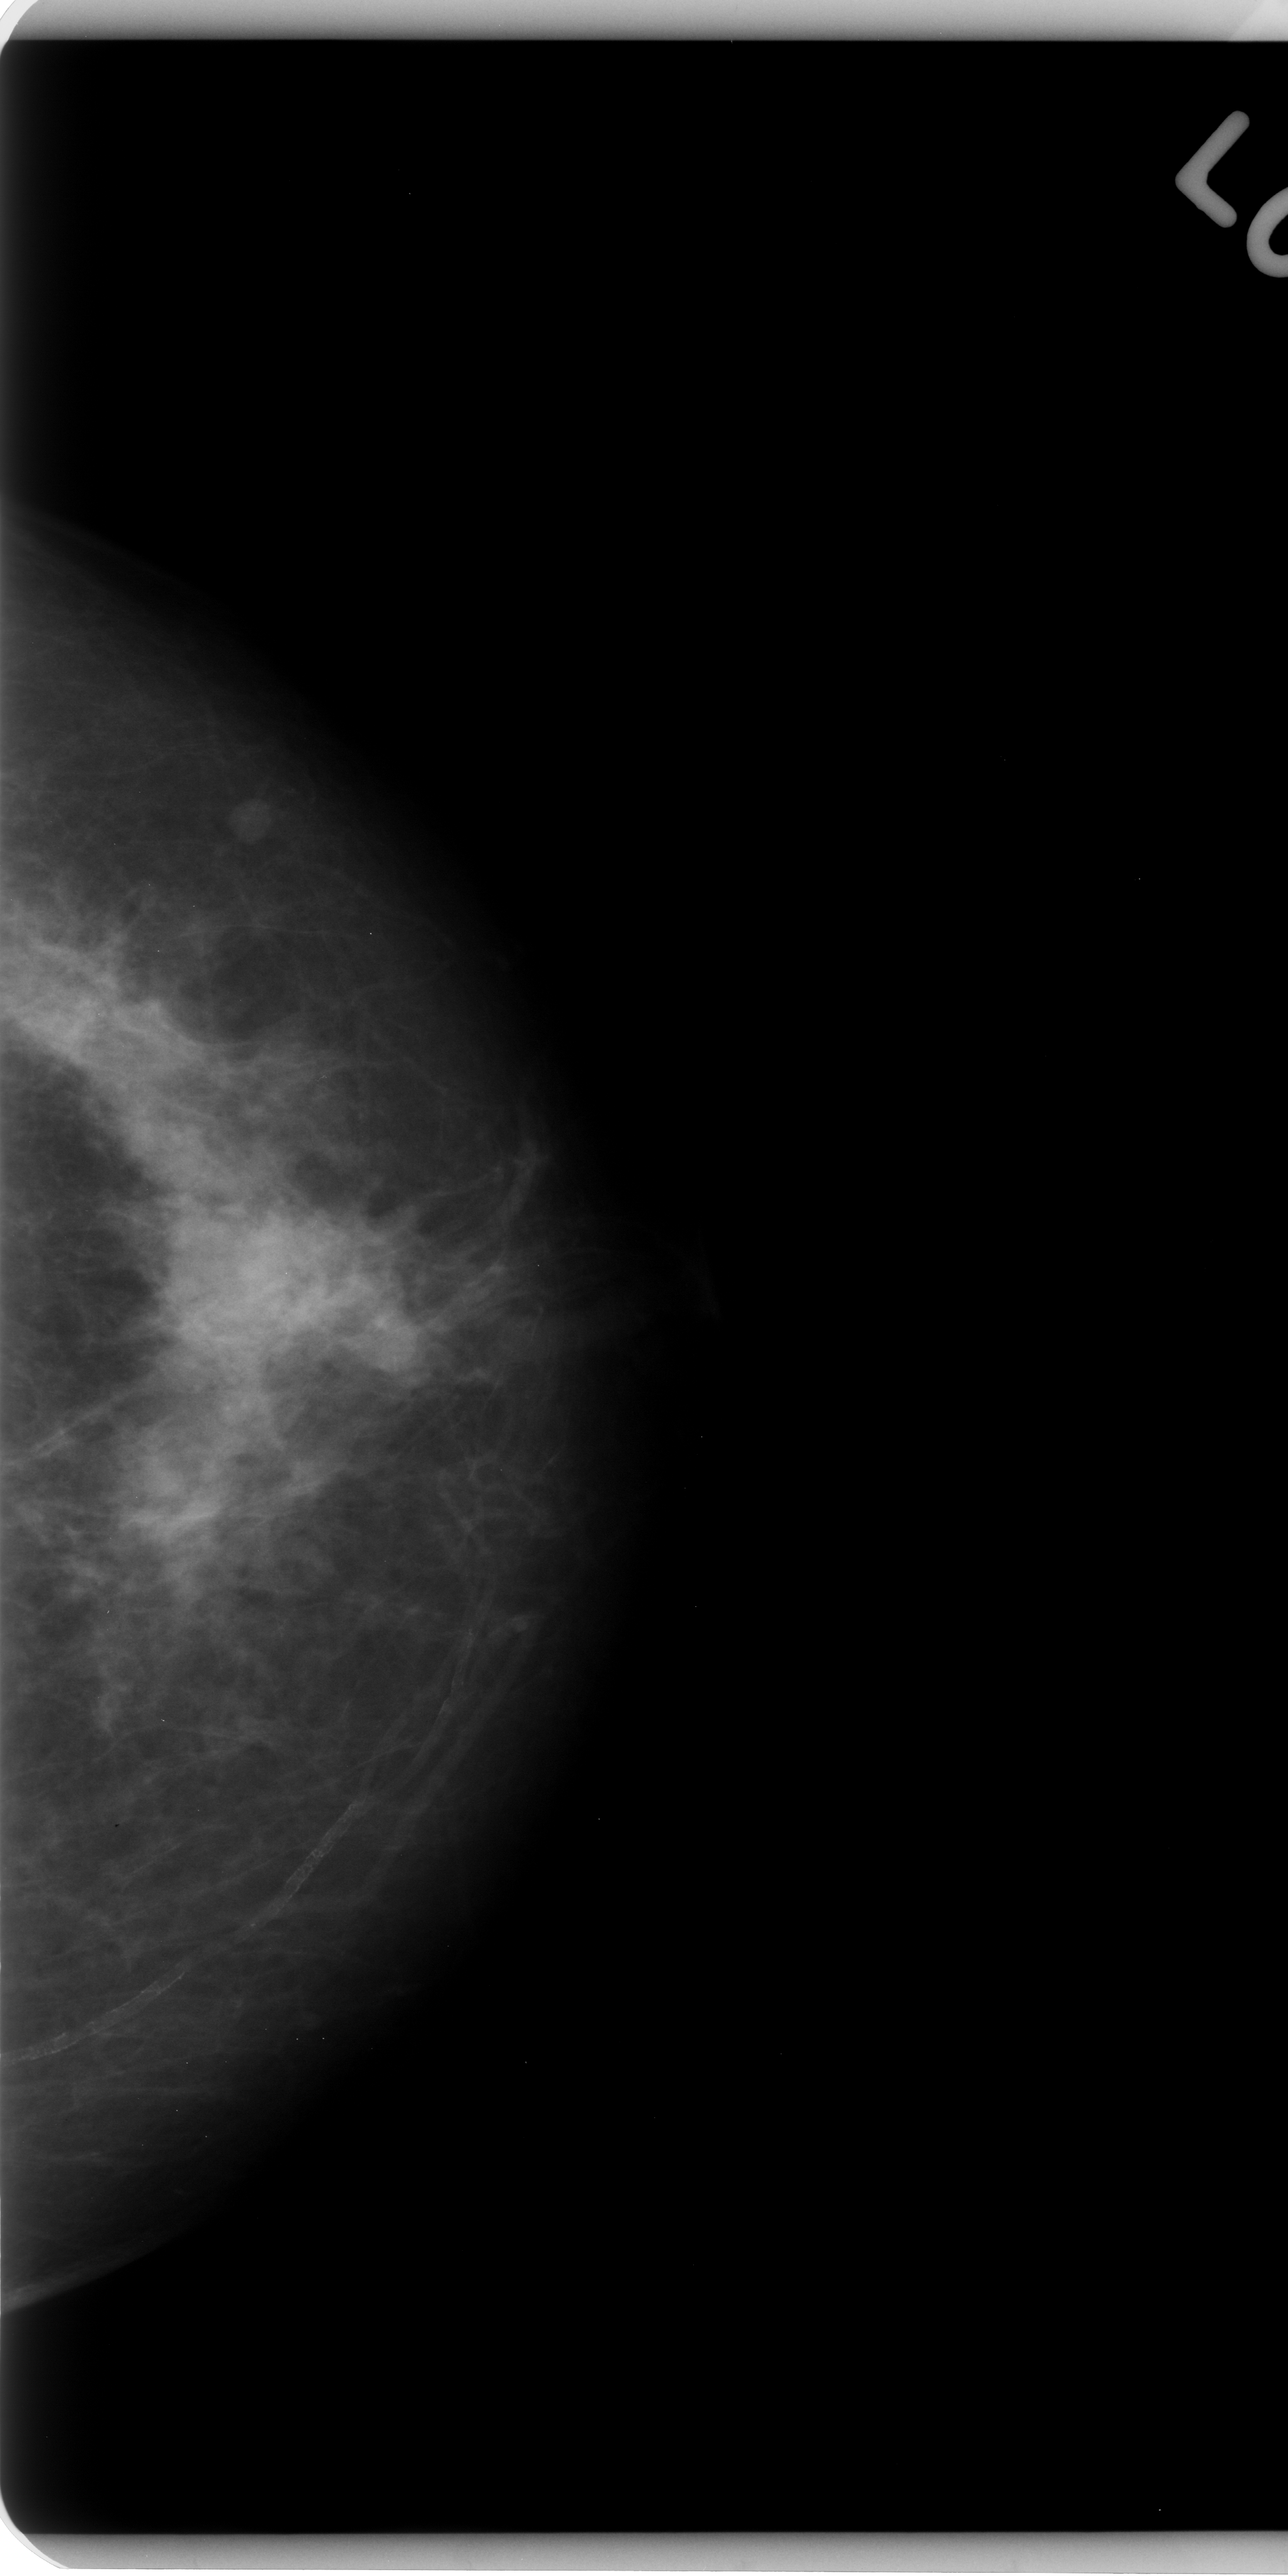
Scanned film-screen mammogram, left breast, CC view, BI-RADS breast density category 2 (scale 1–4).
Abnormality record for this image: mass, shape irregular, margins ill defined; BI-RADS assessment category 4; subtlety rating 2 on a 1 (subtle) to 5 (obvious) scale; pathology (as recorded): benign.